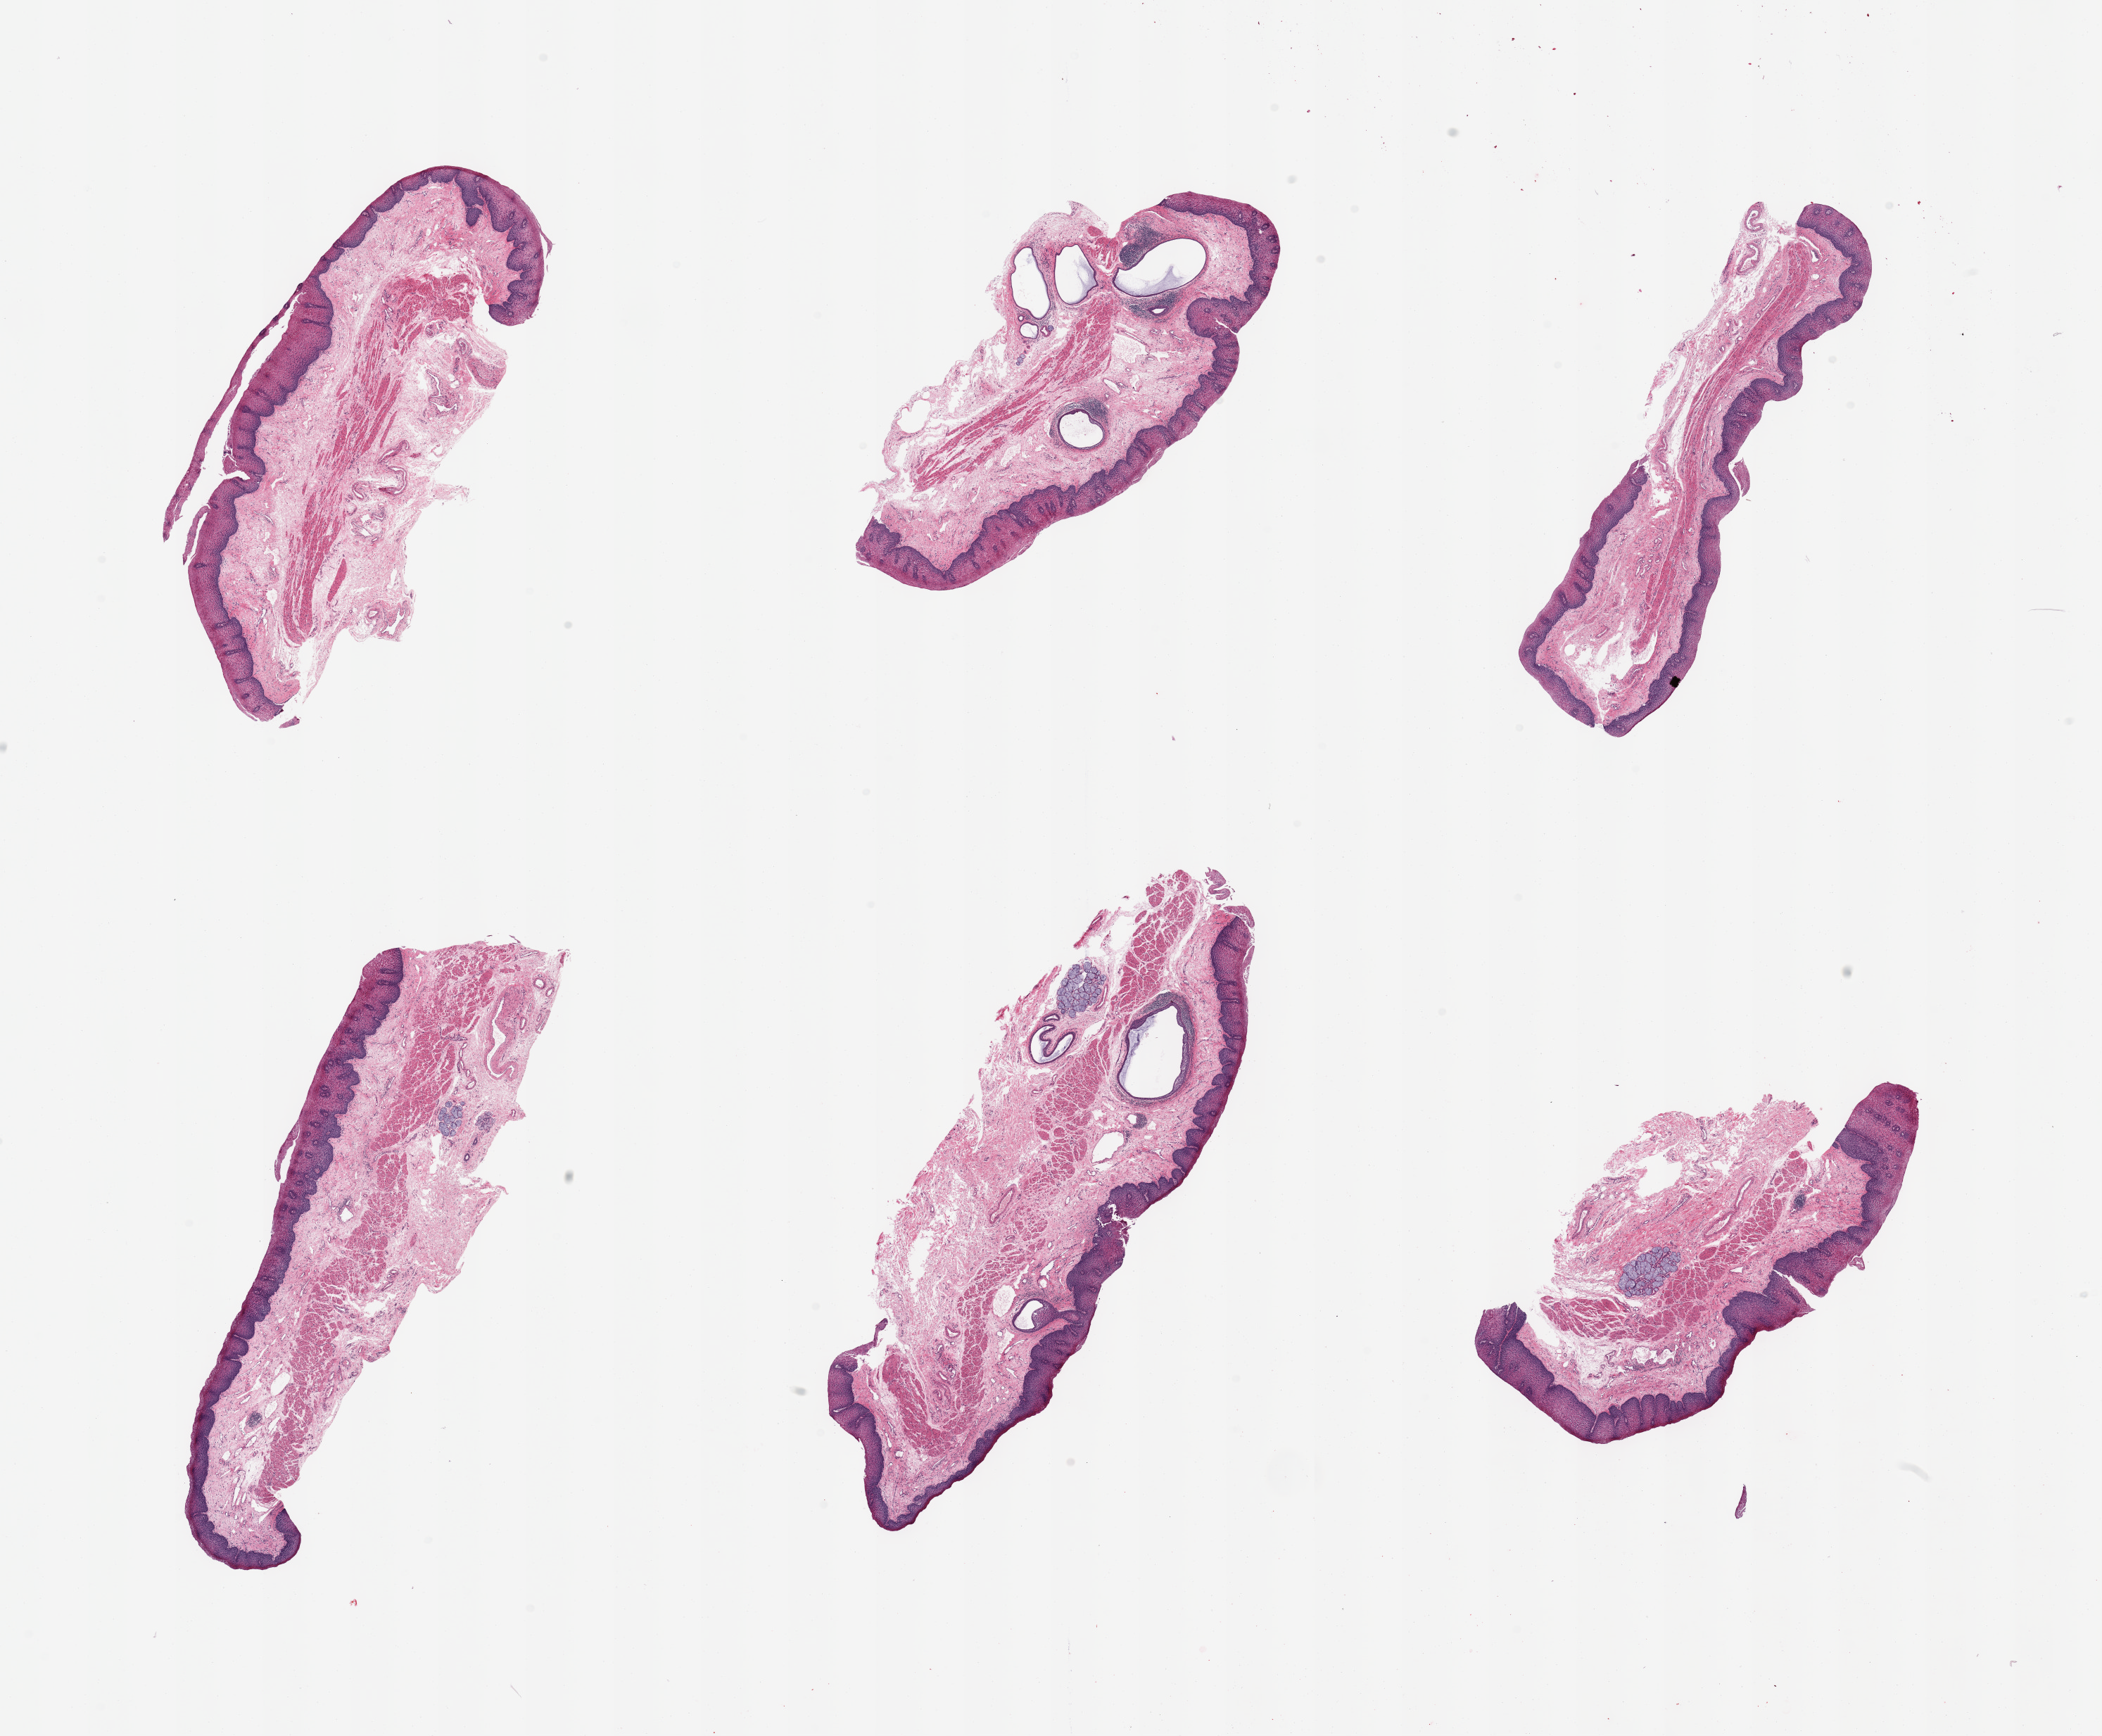
Whole-slide image, hematoxylin and eosin (H&E) stain, low-resolution overview of the scanned area, about 23.6 x 19.5 mm, PAXgene-fixed paraffin-embedded (PFPE) section, section of esophageal mucous membrane (target tissue), donor tissue sample. Male donor.
Review note (as recorded): 6 pieces squamous mucosa up to ~0.4mm, ~15% of thckness; Submucosal mucus glands present.